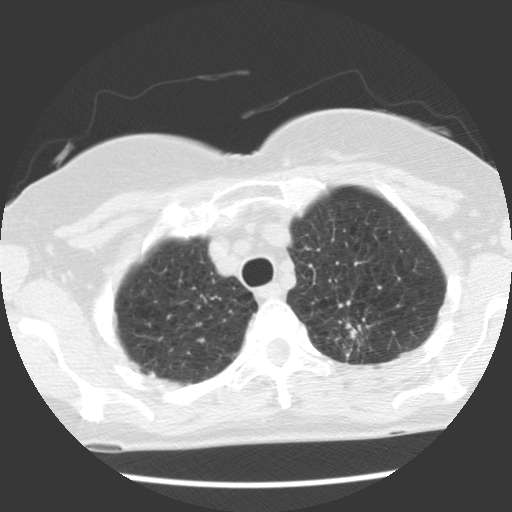
Low-dose screening chest CT, one axial slice; slice 96 of 120 in the series (ordered by position); reconstruction kernel STANDARD; 140 kVp; lung window (W 1500 / L -600 HU); 2.5 mm slice thickness; 512 × 512 image matrix, field of view 300 × 300 mm.
Annotated regions visible in this slice (expert manual segmentation):
- lesion 1 (tumor, upper lobe of left lung): bounding box (x1, y1, x2, y2) in pixels: (350, 329, 357, 339)